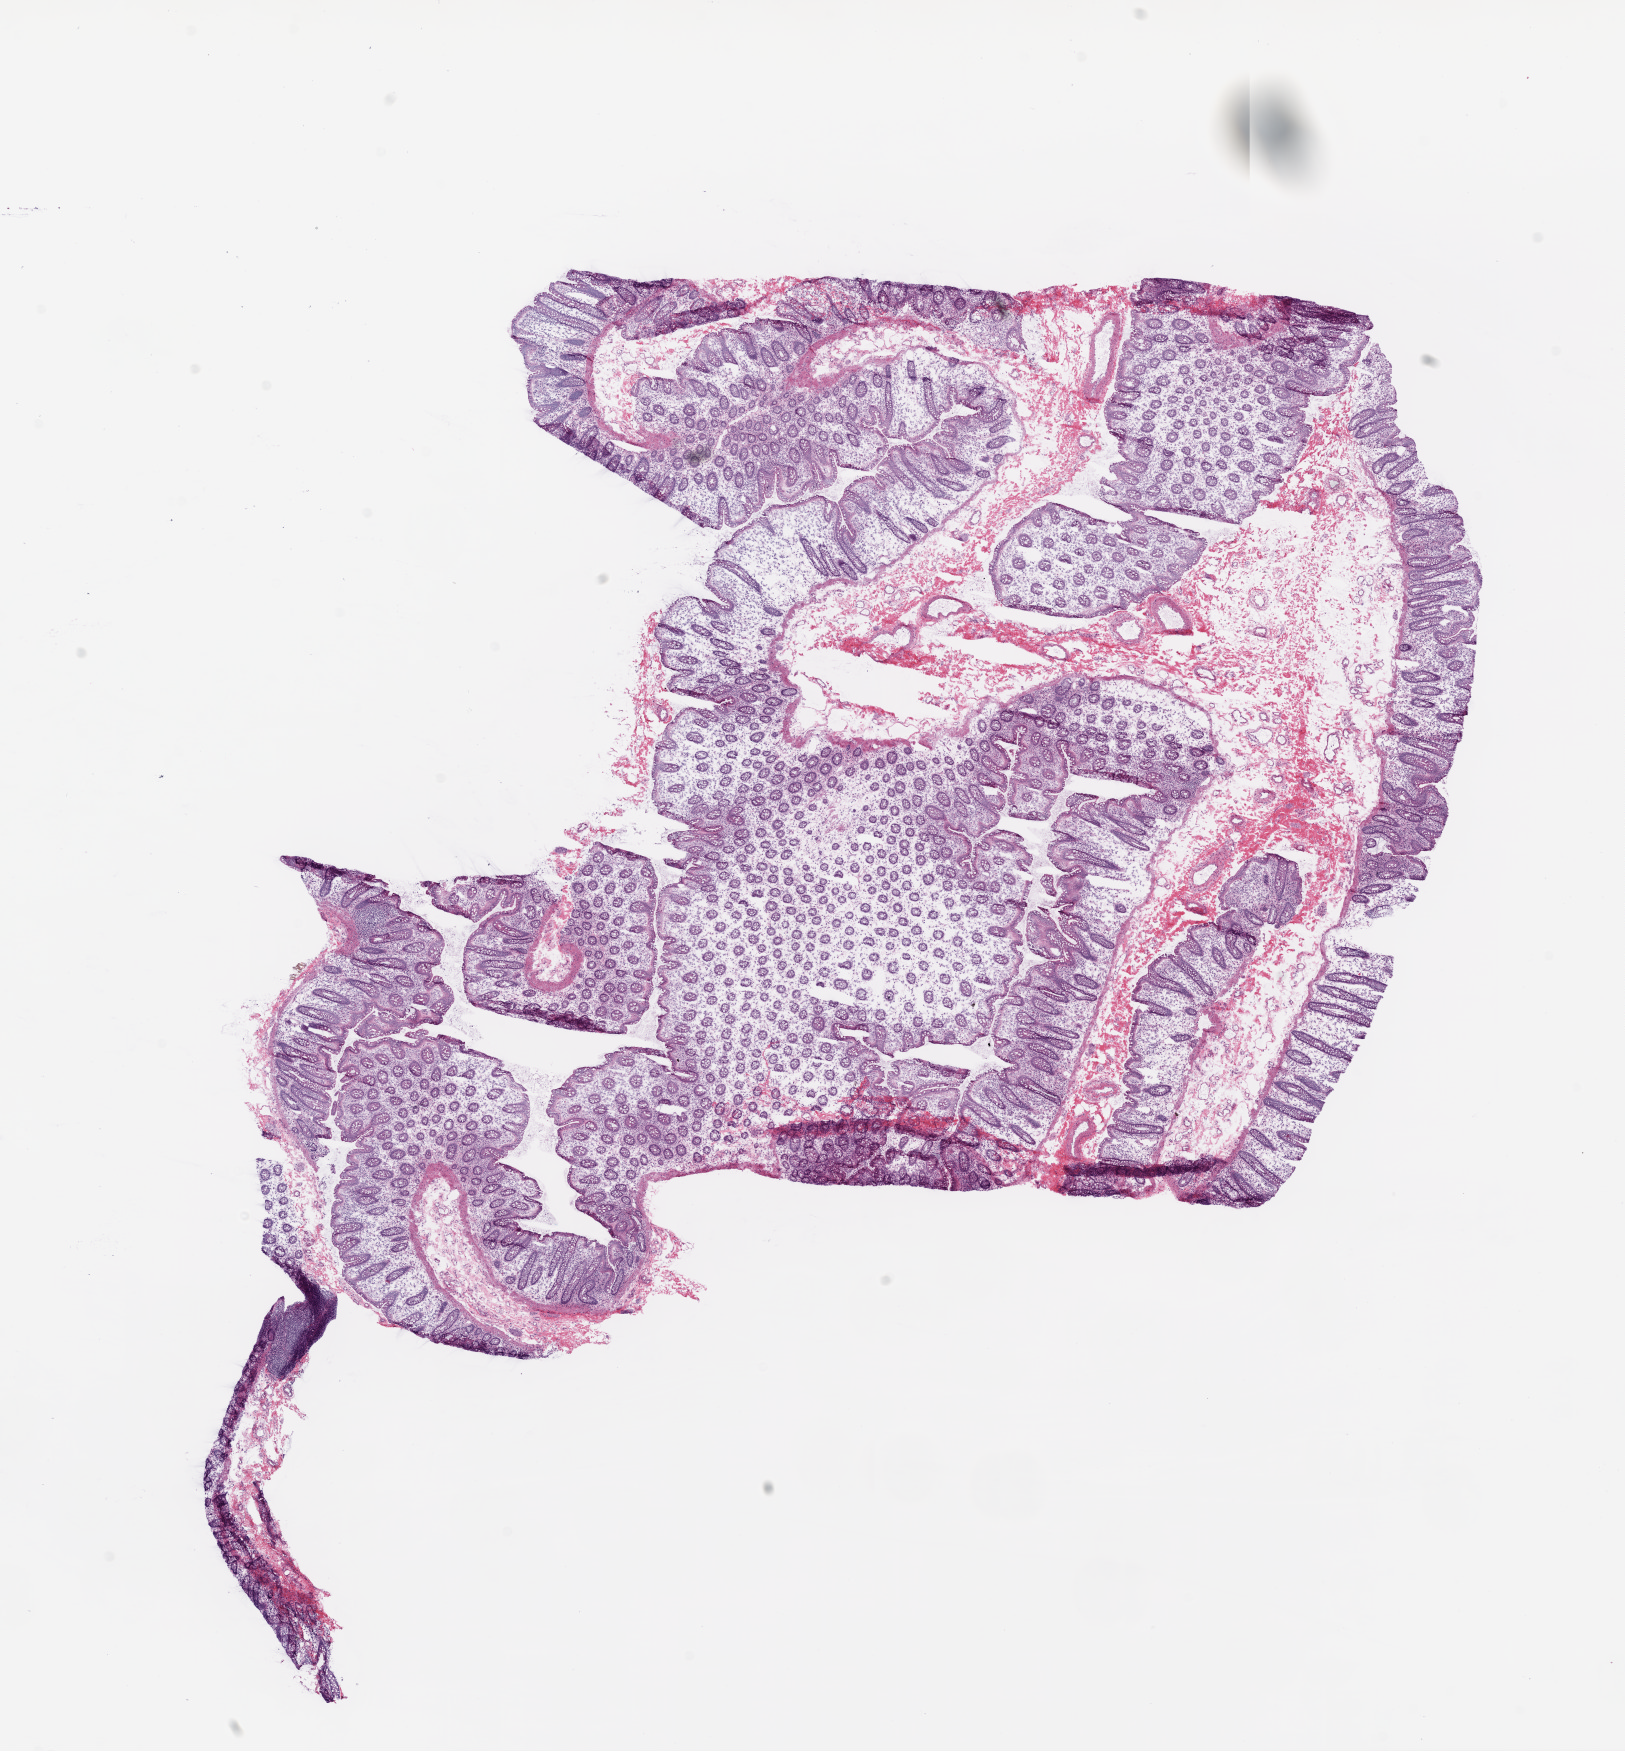
H&E whole-slide image, whole scanned area (about 13.0 x 14.1 mm, acquisition: 20x scan) shown as a low-resolution overview; frozen section from the bottom of the tissue portion; solid tissue normal (non-tumour tissue) sample from the colon. Male patient; age at initial diagnosis 73 years.
This section: solid tissue normal (non-tumour) sample from the same patient. Patient diagnosis: Adenocarcinoma, NOS.